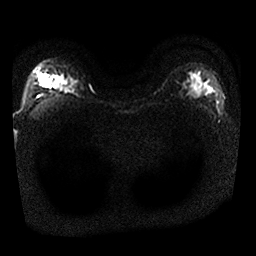
Breast MRI, one axial slice. Position 21 of 25 along the scan axis. Diffusion-weighted series; image 2 of 4 stored at this slice position (different b-values; order by instance number). 1.5 T. 4 mm slice thickness. 256 × 256 image matrix, field of view 340 × 340 mm. Female patient.
Structures marked on this image (expert manual segmentation):
- tumour on diffusion-weighted imaging: bounding box [x1, y1, x2, y2] px = [40, 75, 51, 86]